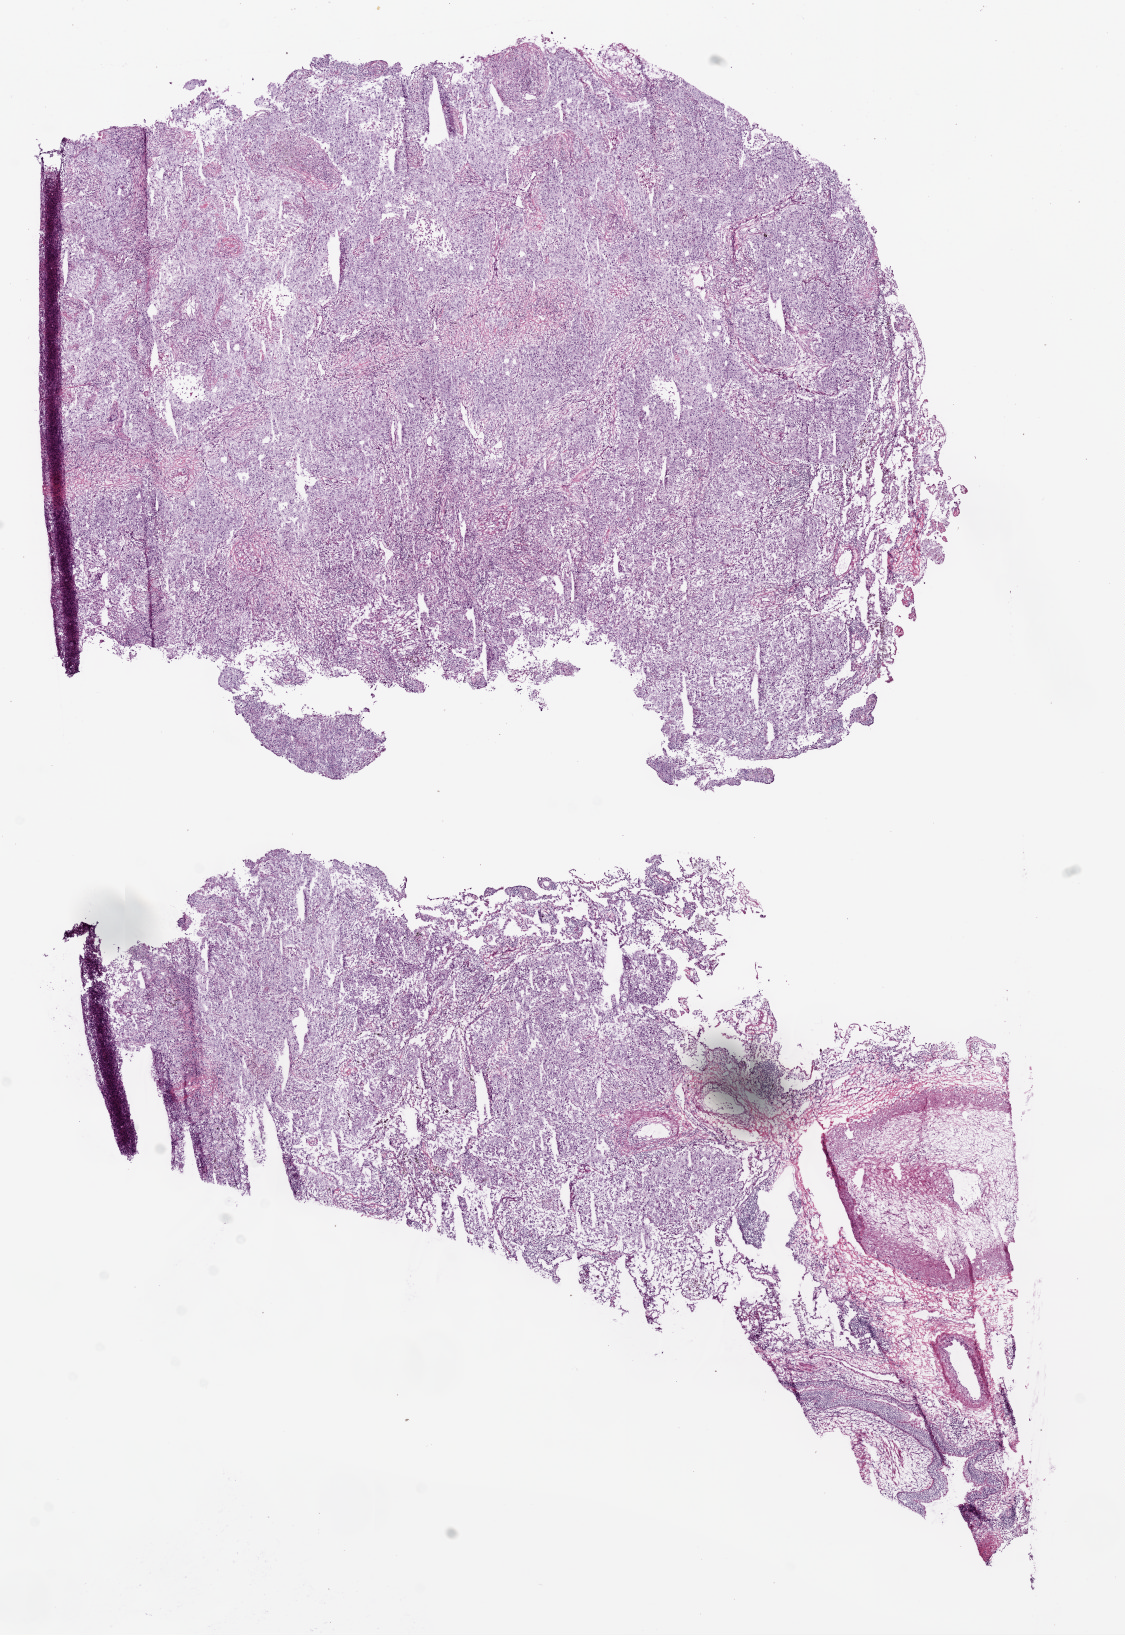
Hematoxylin and eosin (H&E) stained whole-slide image, a low-resolution overview of the entire scanned area, about 9.0 x 13.1 mm; frozen section from the bottom of the tissue portion; lung, primary tumour sample. Female, age 69 years at initial diagnosis. Pathologist review of this section (percent, as recorded): tumour cells 65%, tumour nuclei 70%, normal cells 5%, stromal cells 15%, necrosis 10%.
• AJCC pathologic stage: IB
• pathologic diagnosis: Squamous cell carcinoma, NOS (upper lobe, lung)